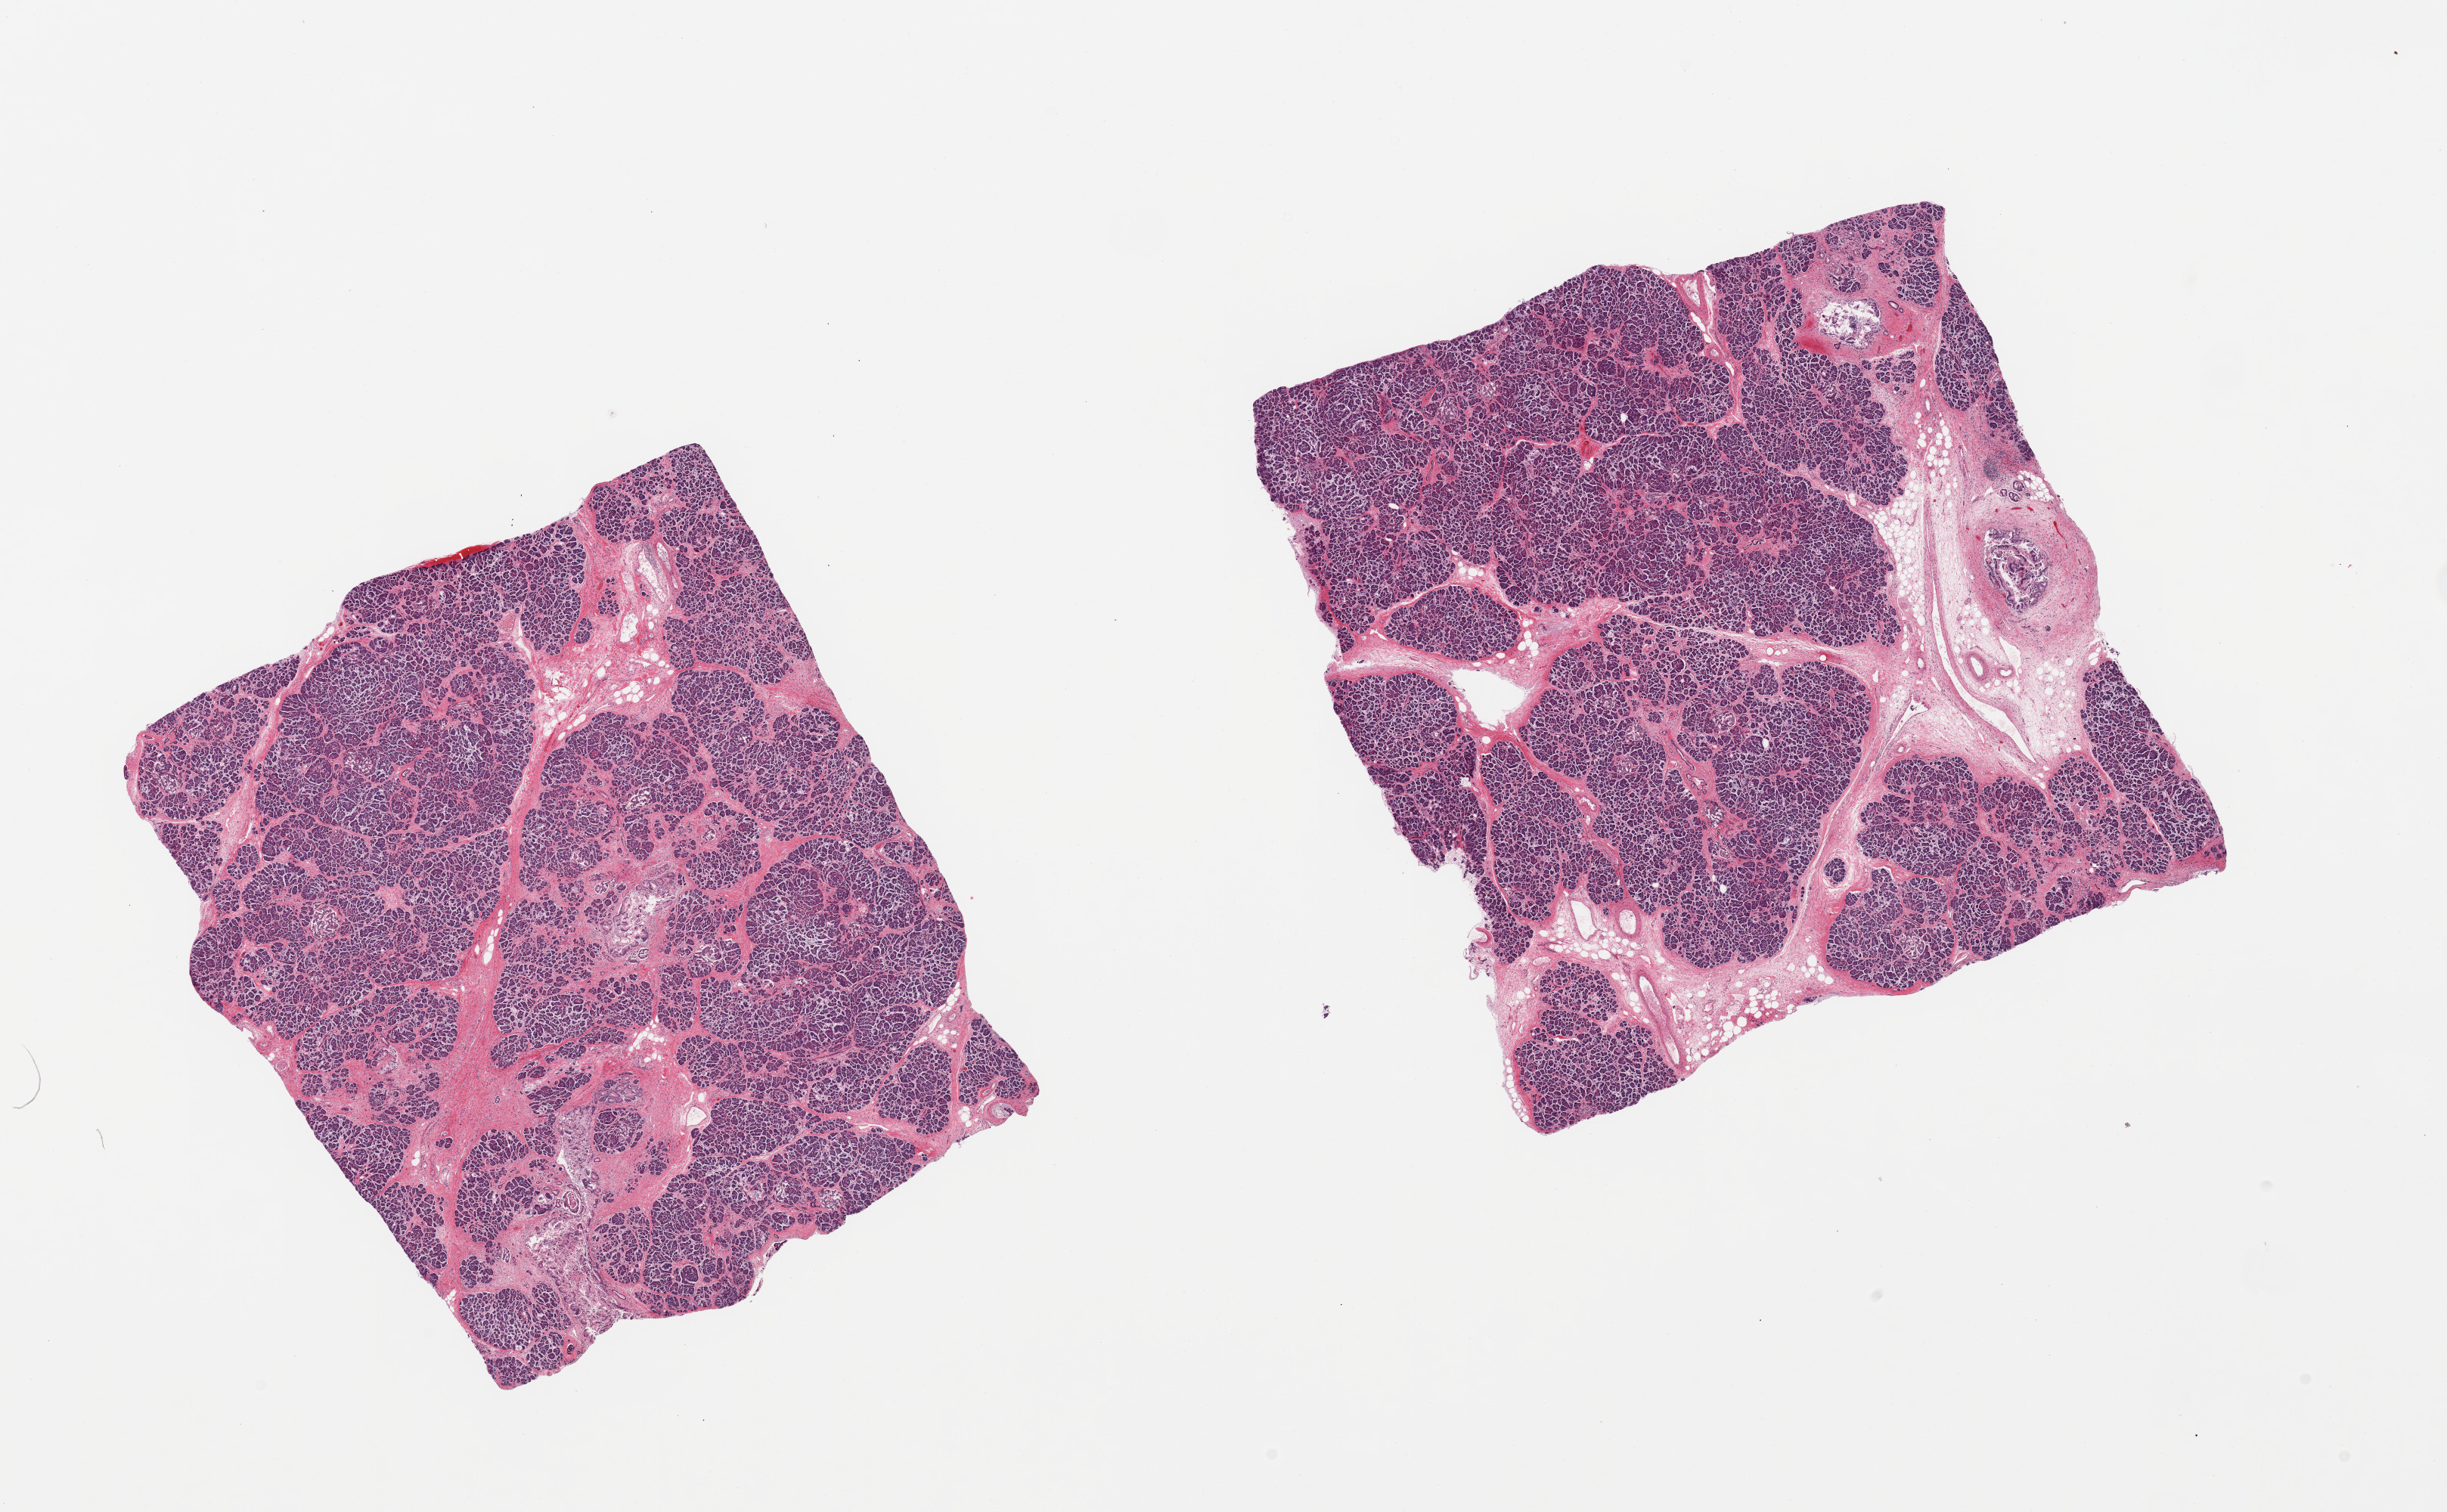
Digitized haematoxylin and eosin-stained section, low-resolution overview of the scanned area, about 25.6 x 15.8 mm (slide scanned at 20x), PAXgene-fixed paraffin-embedded (PFPE) section, target tissue: pancreas, tissue donor sample. Donor: male.
Reviewer comment on this tissue sample: 2 pieces; interlobular and acinar fibrosis, islets visualized, some atrophy, sloughing of ductal epithelium with ?PanIN, 5-15% is fat/fibrous.